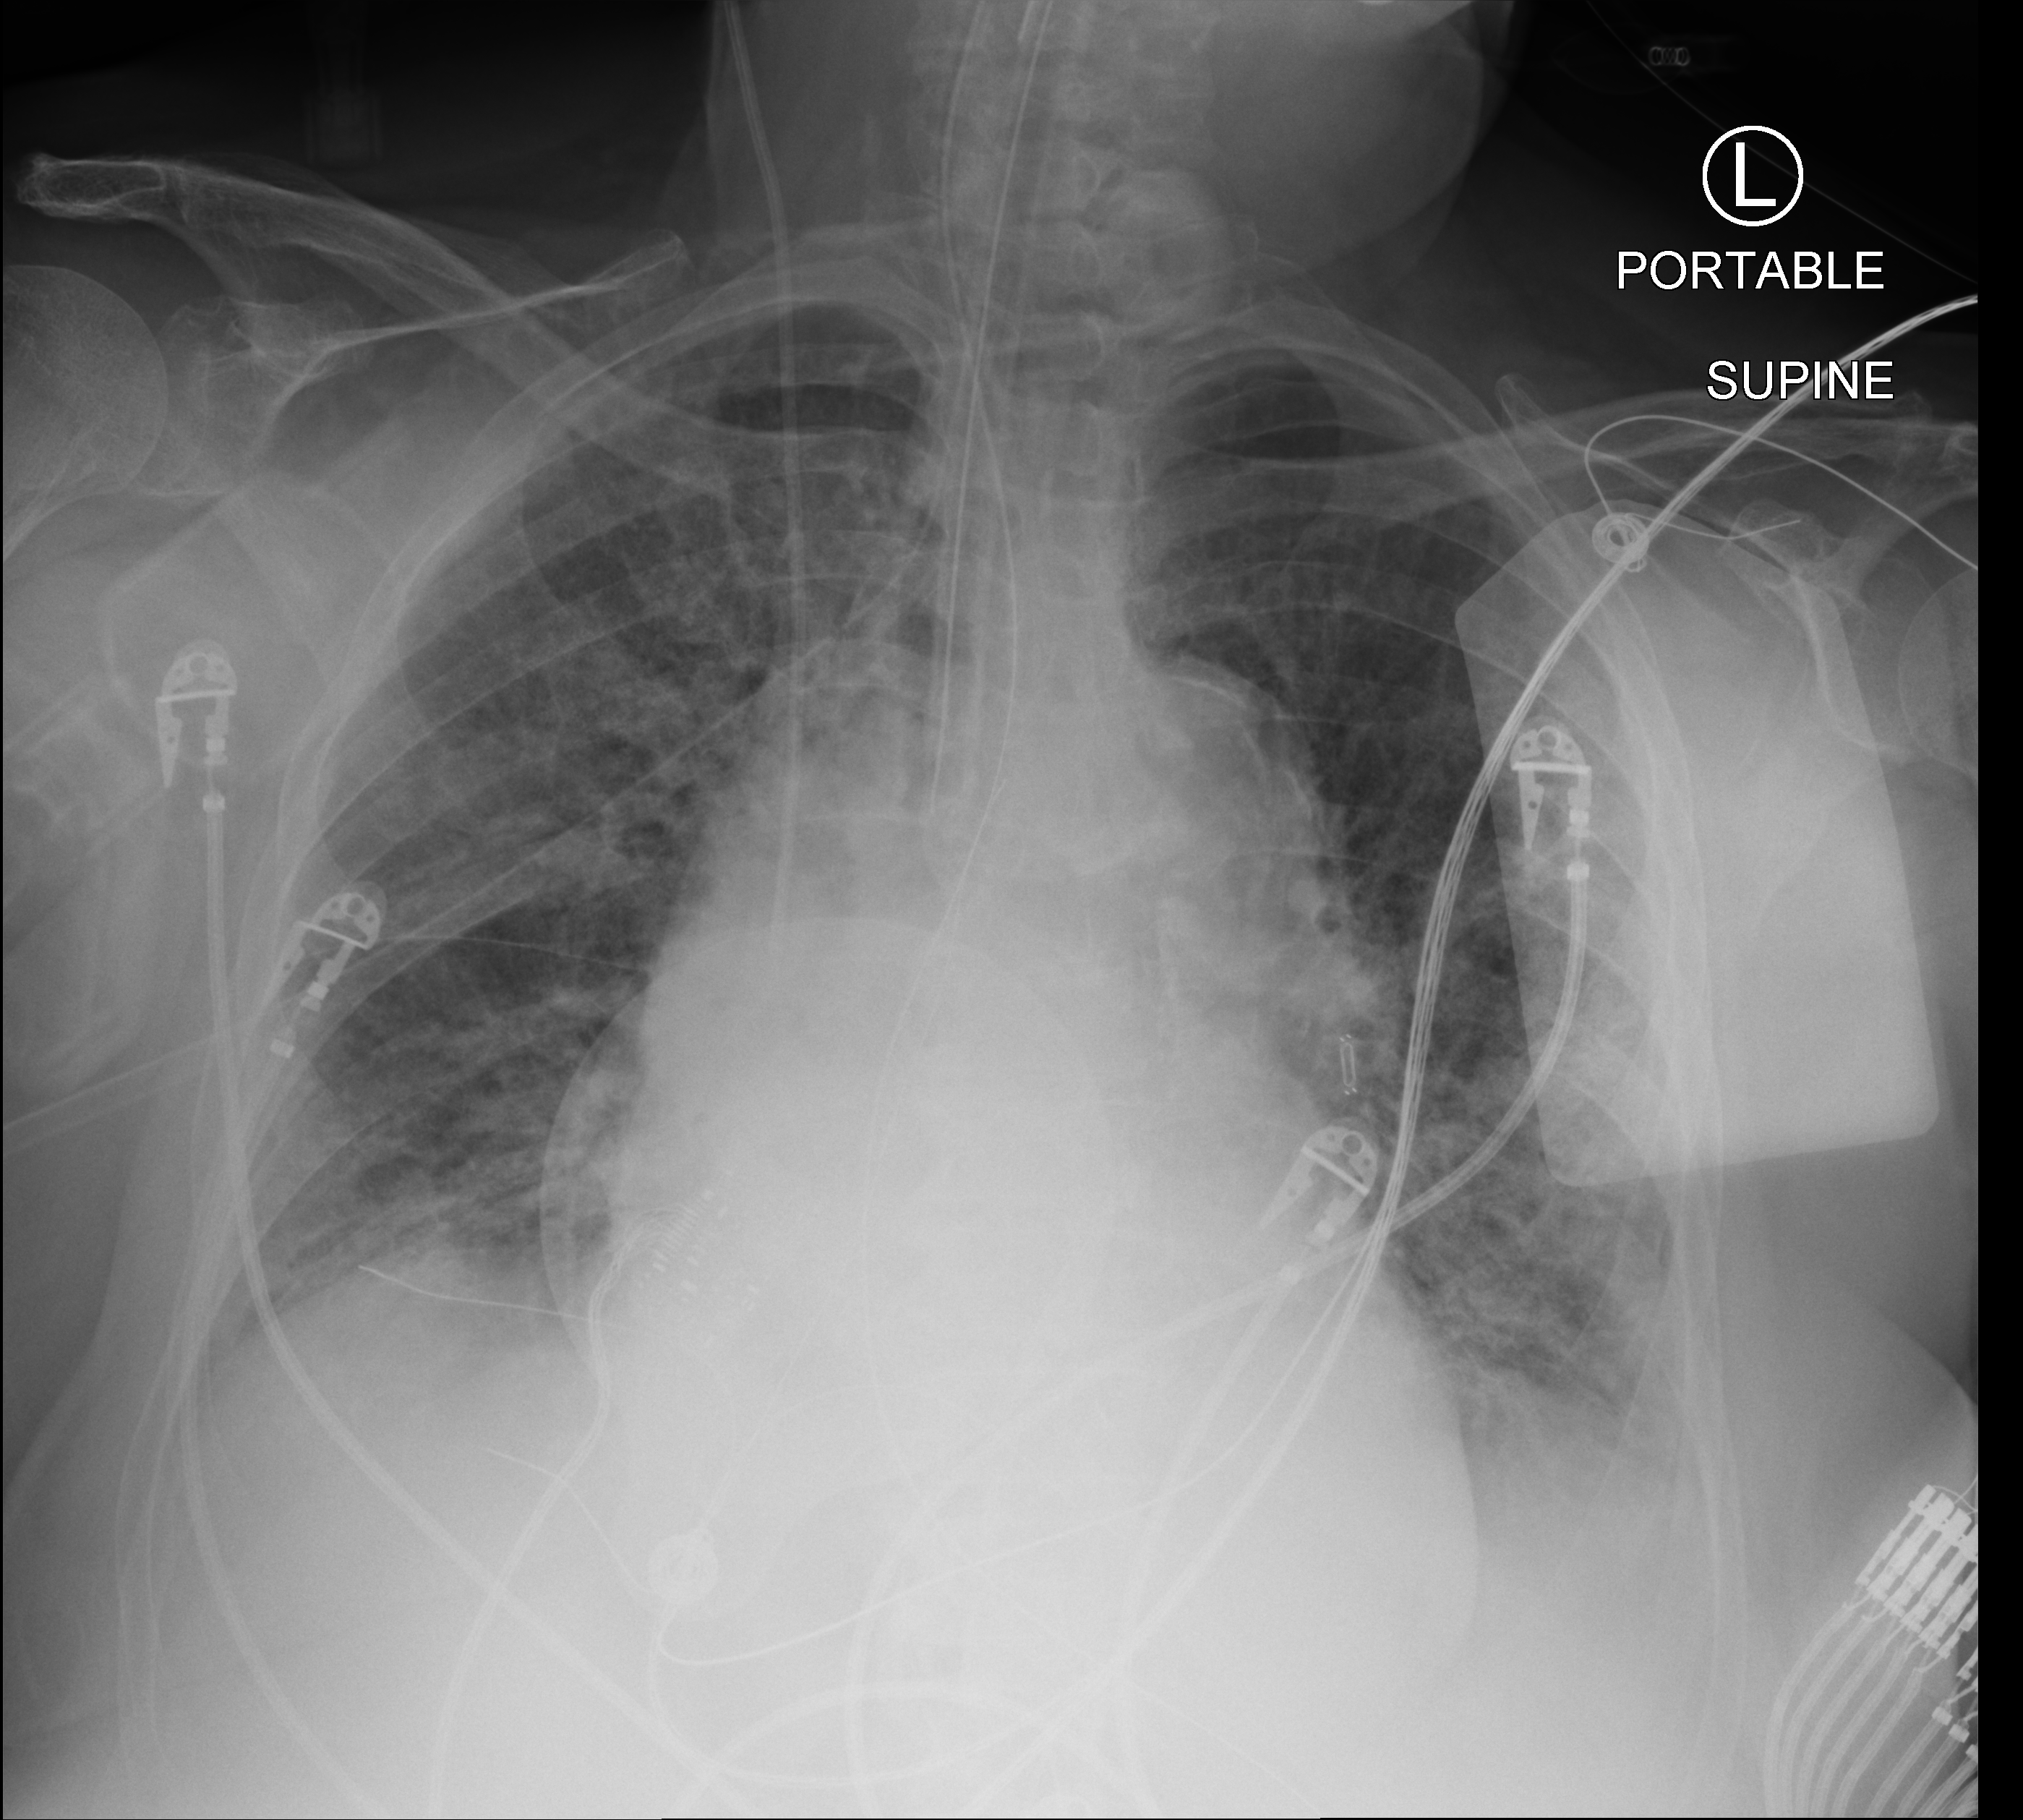
Chest X-ray (portable); anteroposterior (AP) projection. Female patient hospitalised with COVID-19, age 75–90 years.
From the hospital-stay record, not from the radiograph (when in the stay this image was taken is not recorded): hypertension (admission record): yes.